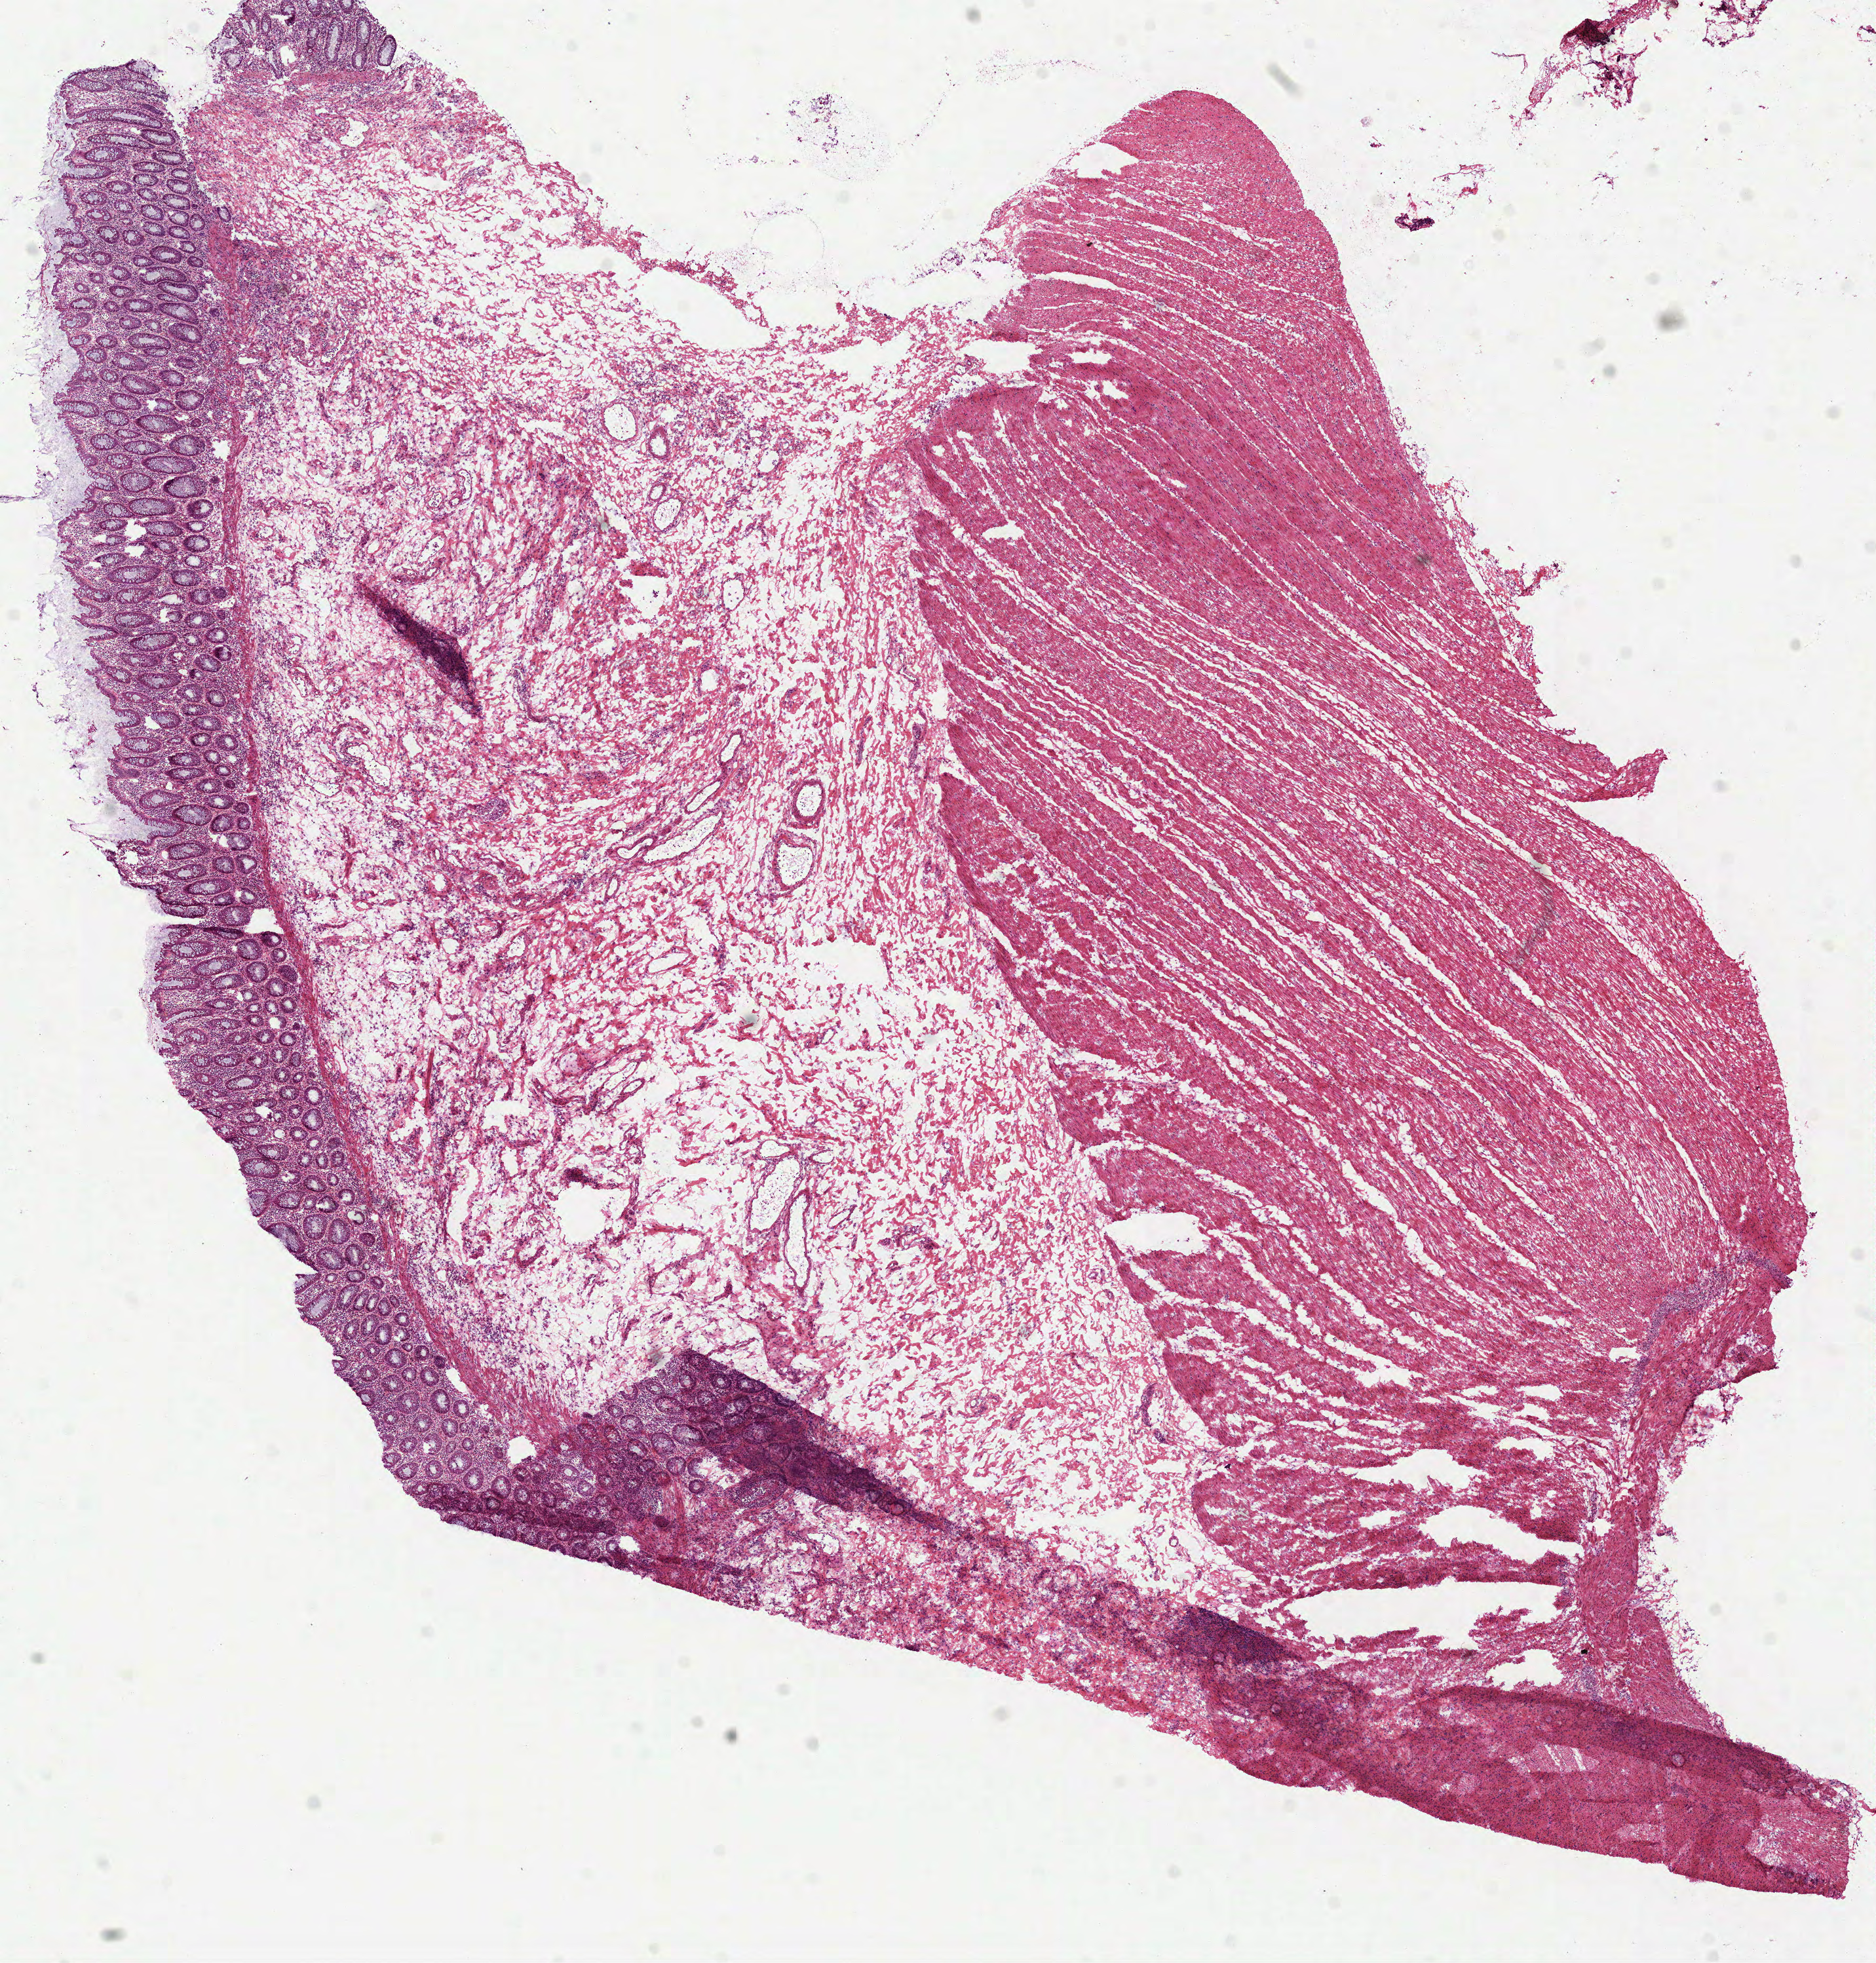
Digitized Hematoxylin and eosin (H&E) stained tissue section (whole slide), a low-resolution overview of the entire scanned area, about 11.5 x 12.1 mm (slide scanned at 40x); frozen section; sample: solid tissue normal (non-tumour tissue), colon. Female patient; age at initial diagnosis 77 years.
* this section: solid tissue normal (non-tumour) sample from the same patient
* patient diagnosis: Adenocarcinoma, NOS (sigmoid colon)